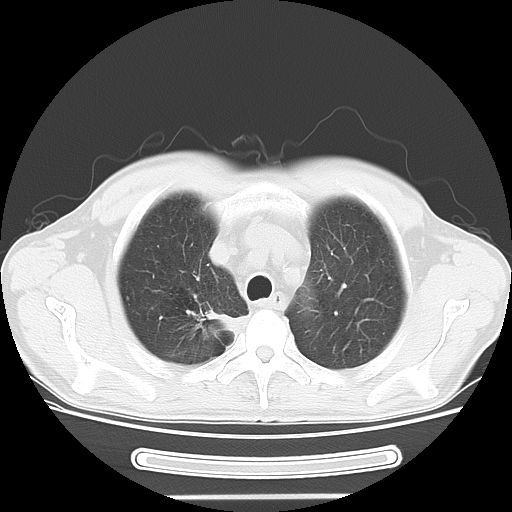
Chest CT, one axial slice; slice 40 of 51 in the series (ordered by position); 120 kVp; lung window (W 1500 / L -600 HU); 5 mm slice thickness; 512 × 512 image matrix. Male patient, age 57 years. From the clinical record (not read from this slice): clinical TNM (as recorded): T2 N3 M1b.
Annotated regions visible in this slice (bounding box drawn by a radiologist):
- lung tumour (recorded histology: adenocarcinoma): bounding box (x1, y1, x2, y2) in pixels: (207, 305, 240, 336)